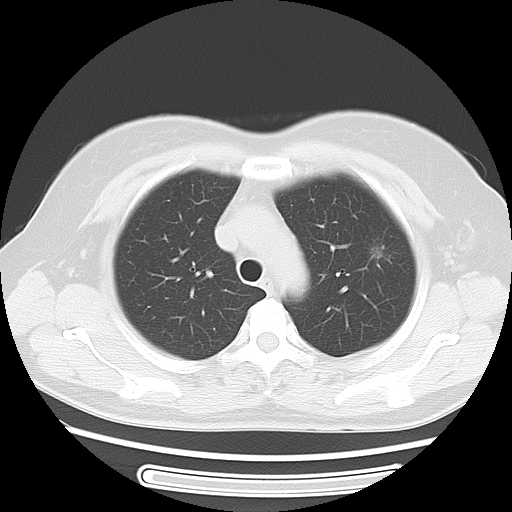
Chest CT, one axial slice. Position 38 of 52 along the scan axis. Reconstruction kernel LUNG. 120 kVp. Lung window (W 1500 / L -600 HU). 5 mm slice thickness. 512 × 512 image matrix, field of view 350 × 350 mm. Female patient, age 54 years. From the clinical record (not read from this slice): clinical TNM (as recorded): T1c N0 M0.
Outlined on this slice (bounding box drawn by a radiologist):
- lung tumour (recorded histology: adenocarcinoma): box from (x=367, y=234) to (x=395, y=269) px